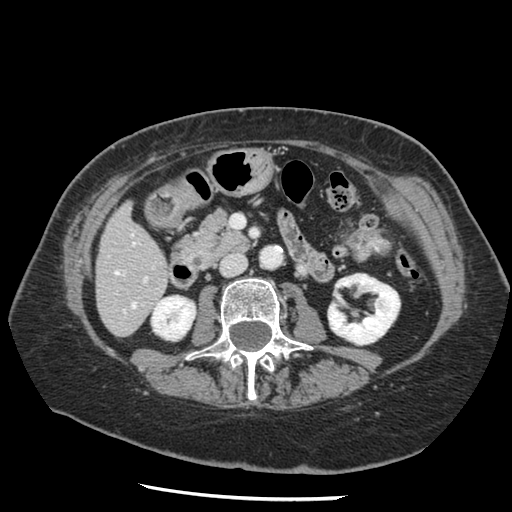
Contrast-enhanced abdominal CT, one axial slice; position 45 of 148 along the scan axis; 120 kVp; intravenous contrast given; soft-tissue window (W 400 / L 40 HU); 512 × 512 image matrix, field of view 330 × 330 mm. Female patient, age 85 years. Case-level facts recorded for this patient, not image findings: diagnosis: colorectal cancer liver metastases, imaged before liver resection; multiple liver metastases: no; largest metastasis: 0.9 cm; disease in both lobes: no.
Annotated regions visible in this slice (outlined manually by an expert reader):
- hepatic veins: bounding box <115,271,136,308> (left, top, right, bottom; pixels)
- liver: <96,205,169,336>
- planned liver remnant (the part of the liver to remain after resection): <96,205,169,330>